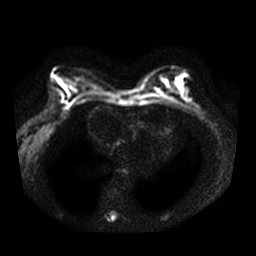
Breast MRI, one axial slice. Position 16 of 38 along the scan axis. Diffusion-weighted series; image 2 of 4 stored at this slice position (different b-values; order by instance number). 3 T. 5 mm slice thickness. 256 × 256 image matrix. Female patient.
Annotated regions visible in this slice (outlined manually by an expert reader):
- tumour on diffusion-weighted imaging: bounding box <176,81,182,90> (left, top, right, bottom; pixels)